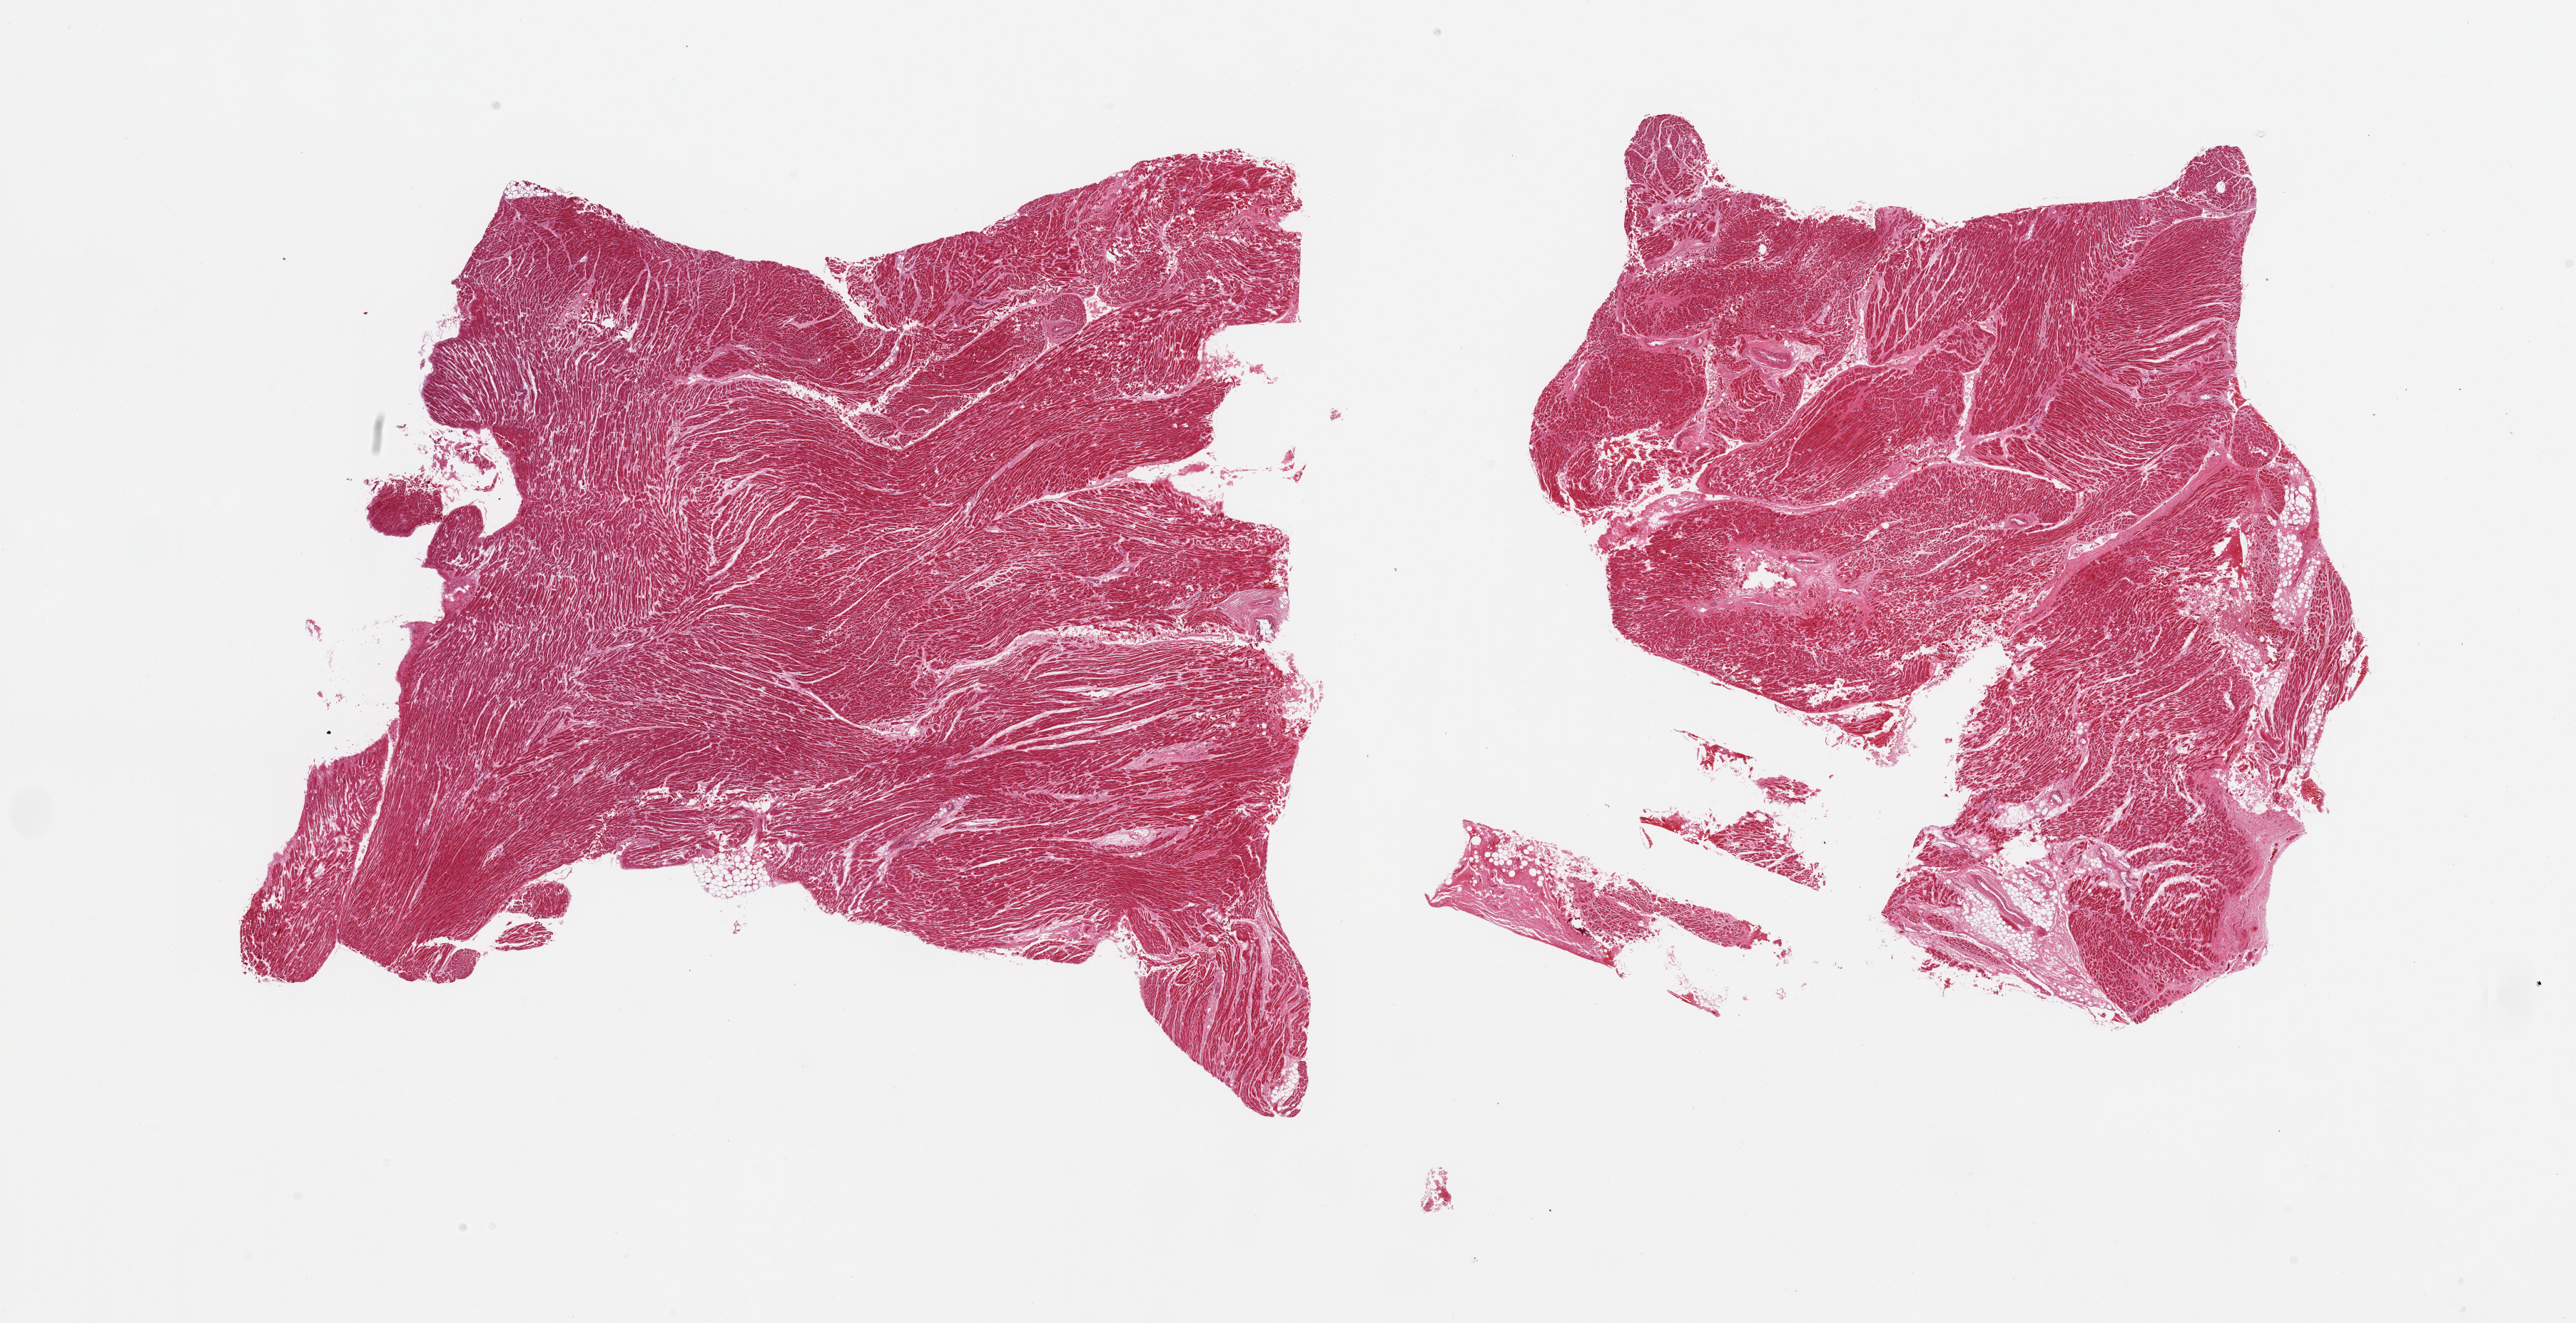
Whole-slide image, hematoxylin and eosin (H&E) stain, shown as a low-resolution overview of the whole scanned area (about 28.5 x 14.7 mm, from a 20x scan); PAXgene-fixed, paraffin-embedded tissue; sampled site (target tissue): heart; donor tissue sample. Male donor.
Reviewer comment on this tissue sample: 2 pieces; interstitial fibrosis and scarring, perivascular fat, myocyte hypertrophy.